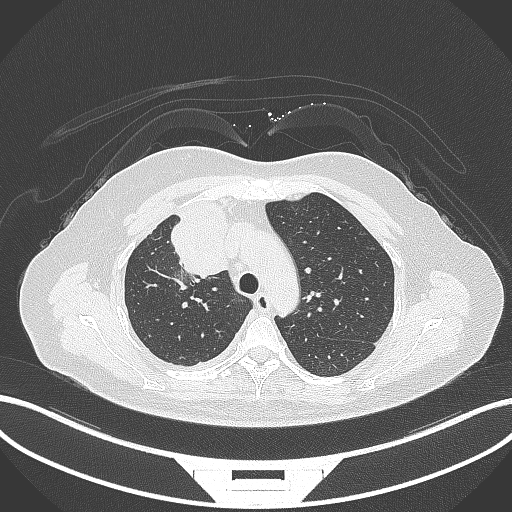
Chest CT, one axial slice; position 218 of 305 along the scan axis; lung window (W 1500 / L -600 HU); 1 mm slice thickness; 512 × 512 image matrix, field of view 400 × 400 mm. Female patient, age 52 years. From the clinical record (not read from this slice): clinical TNM (as recorded): T3 N1 M1.
Outlined on this slice (rectangle marked by the reading radiologist):
- lung tumour (recorded histology: adenocarcinoma): bounding box (x1, y1, x2, y2) in pixels: (166, 197, 230, 279)